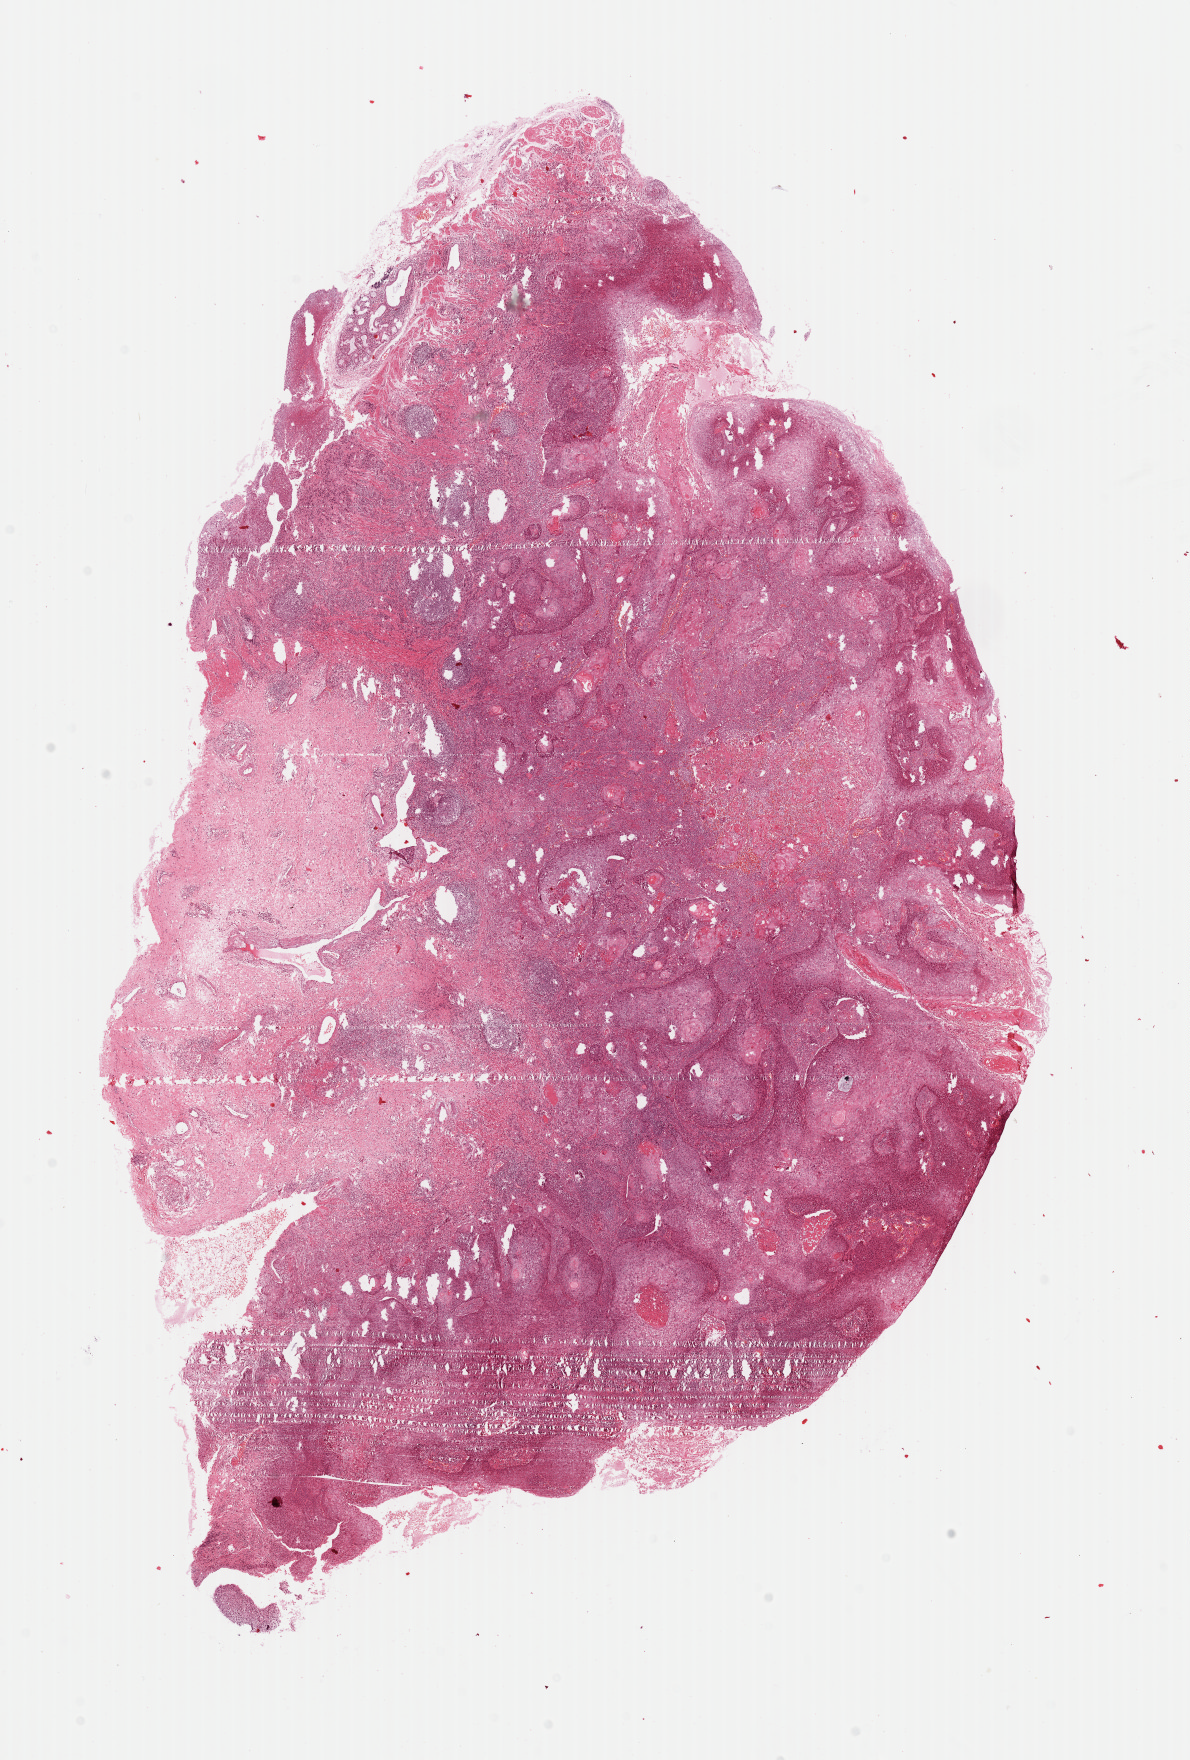
Digitized H&E tissue section (whole slide) — shown as a low-resolution overview of the whole scanned area (about 9.4 x 13.9 mm, acquisition: 40x scan); formalin-fixed paraffin-embedded (FFPE) diagnostic section; esophagus, primary tumour sample. Patient: male, age at initial diagnosis 49 years. Histologic grade: G2 (moderately differentiated).
- histologic diagnosis: Squamous cell carcinoma, NOS
- AJCC pathologic stage: IIA (6th edition)